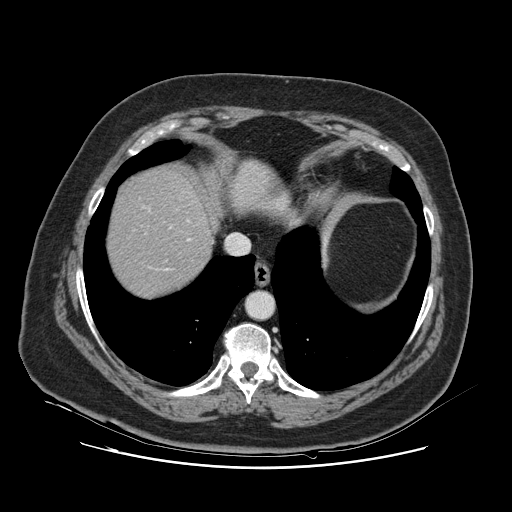
Contrast-enhanced abdominal CT, one axial slice; position 108 of 132 along the scan axis; 120 kVp; intravenous contrast given; soft-tissue window (W 400 / L 40 HU); 512 × 512 image matrix. Female patient, age 73 years. Case-level facts recorded for this patient, not image findings: diagnosis: colorectal cancer liver metastases, imaged before liver resection; multiple liver metastases: no; largest metastasis: 7 cm; disease in both lobes: no.
Structures marked on this image (outlined manually by an expert reader):
- hepatic veins: bounding box <149,210,190,270> (left, top, right, bottom; pixels)
- liver: <109,172,211,296>
- planned liver remnant (the part of the liver to remain after resection): <109,172,211,297>
- portal vein (with intrahepatic branches): <169,226,172,229>